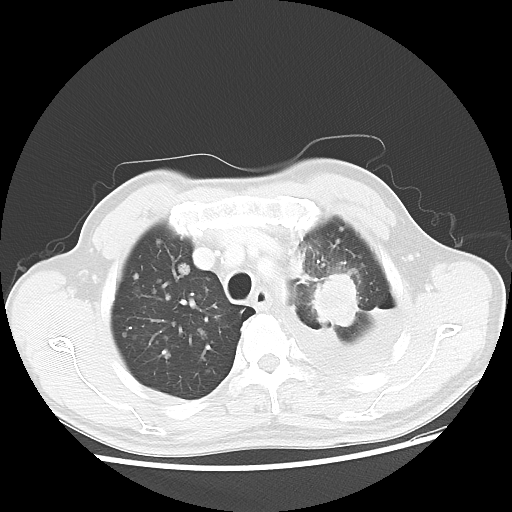
Chest CT, one axial slice. Slice 38 of 47 in the series (ordered by position). Reconstruction kernel LUNG. Lung window (W 1500 / L -600 HU). 512 × 512 image matrix, field of view 362 × 362 mm. Patient: male, 55 years. Case-level facts recorded for this patient, not image findings: clinical TNM (as recorded): T2 N3 M1a.
Structures marked on this image (bounding box drawn by a radiologist):
- lung tumour (recorded histology: squamous cell carcinoma): bounding box [x1, y1, x2, y2] px = [297, 256, 363, 333]